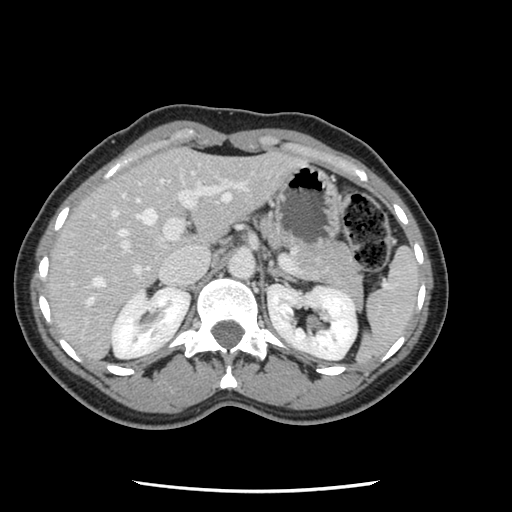
Contrast-enhanced abdominal CT, one axial slice; position 76 of 134 along the scan axis; soft-tissue window (W 400 / L 40 HU); 512 × 512 image matrix, field of view 330 × 330 mm. Female patient, age 43 years. Case-level facts recorded for this patient, not image findings: diagnosis: colorectal cancer liver metastases, imaged before liver resection; multiple liver metastases: yes; largest metastasis: 3.4 cm; disease in both lobes: yes.
Structures marked on this image (manually delineated by an expert):
- hepatic veins: bounding box <87,181,230,305> (left, top, right, bottom; pixels)
- liver: <48,149,298,360>
- planned liver remnant (the part of the liver to remain after resection): <47,152,188,304>
- portal vein (with intrahepatic branches): <72,180,246,294>